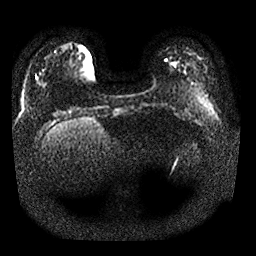
Breast MRI, one axial slice. Position 3 of 25 along the scan axis. Diffusion-weighted series; image 2 of 4 stored at this slice position (different b-values; order by instance number). 1.5 T. 256 × 256 image matrix, field of view 350 × 350 mm. Female patient.
Outlined on this slice (expert manual segmentation):
- tumour on diffusion-weighted imaging: bounding box (x1, y1, x2, y2) in pixels: (172, 62, 176, 68)